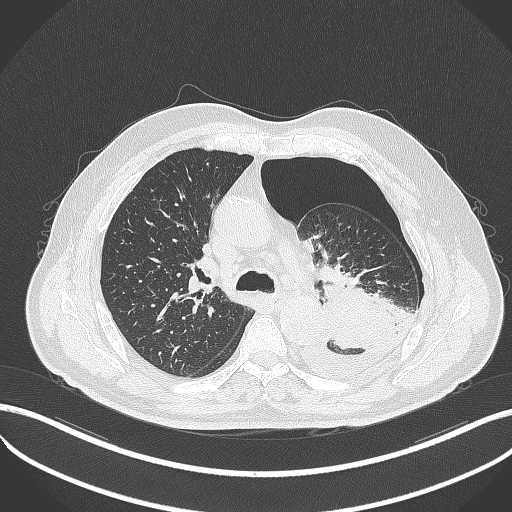
Chest CT, one axial slice. Slice 340 of 464 in the series (ordered by position). Reconstruction kernel B70f. 120 kVp. Lung window (W 1500 / L -600 HU). 512 × 512 image matrix, field of view 400 × 400 mm. Male patient, age 76 years. From the clinical record (not read from this slice): clinical TNM (as recorded): T3 N0 M1b.
Annotated regions visible in this slice (bounding box drawn by a radiologist):
- lung tumour (recorded histology: adenocarcinoma): bounding box <320,271,399,350> (left, top, right, bottom; pixels)